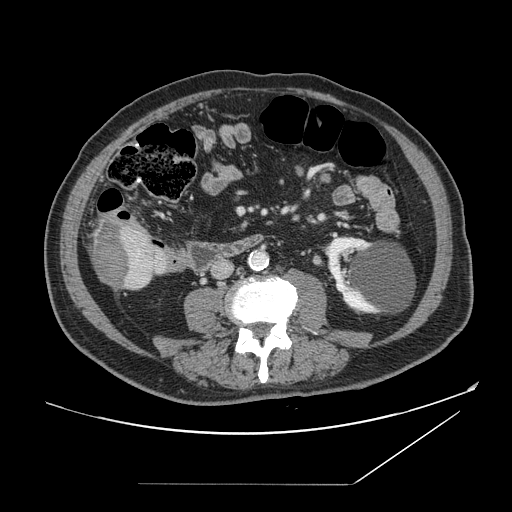
Contrast-enhanced abdominal CT, one axial slice. Position 32 of 166 along the scan axis. Intravenous contrast given. Soft-tissue window (W 400 / L 40 HU). 2.5 mm slice thickness. 512 × 512 image matrix, field of view 416 × 416 mm. Male patient, age 80 years. From the clinical record (not read from this slice): diagnosis: colorectal cancer liver metastases, imaged before liver resection; multiple liver metastases: no; largest metastasis: 2.2 cm; disease in both lobes: no.
Structures marked on this image (manually delineated by an expert):
- liver: bounding box <90,220,163,290> (left, top, right, bottom; pixels)
- liver metastasis: <93,223,132,288>